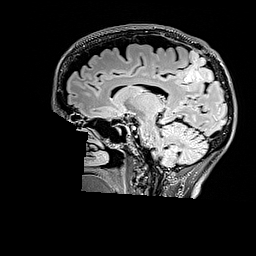
Brain MRI from a brain-tumour surgery series, one sagittal slice; slice 101 of 176 in the series (ordered by position); T2 FLAIR; 1 mm slice thickness; 256 × 256 image matrix, field of view 256 × 256 mm. From the clinical record (not read from this slice): histopathology: Astrocytoma; WHO grade: 3; IDH mutation: yes; tumour location: Right Parietal.
Structures marked on this image (expert manual segmentation):
- tumour: bounding box [x1, y1, x2, y2] px = [184, 50, 213, 82]
- tumour: [184, 58, 214, 83]